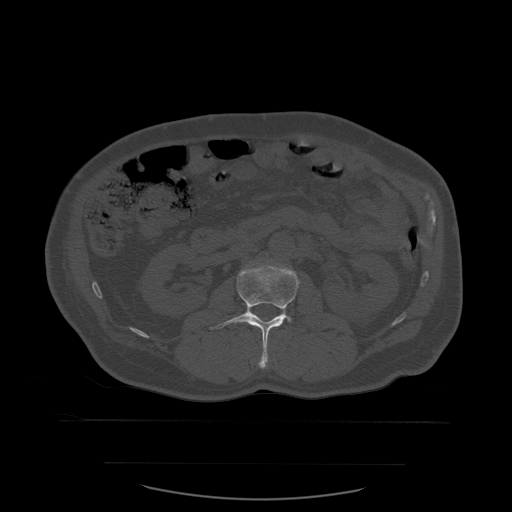
CT including the spine, one axial slice. Slice 217 of 590 in the series (ordered by position). Bone window (W 1800 / L 400 HU). 512 × 512 image matrix, field of view 479 × 479 mm. Patient age 71 years. From the clinical record (not read from this slice): primary cancer: lung.
Annotated regions visible in this slice (semi-automatic segmentation, software-assisted and operator-edited):
- L2 vertebra: bounding box <210,264,300,369> (left, top, right, bottom; pixels)